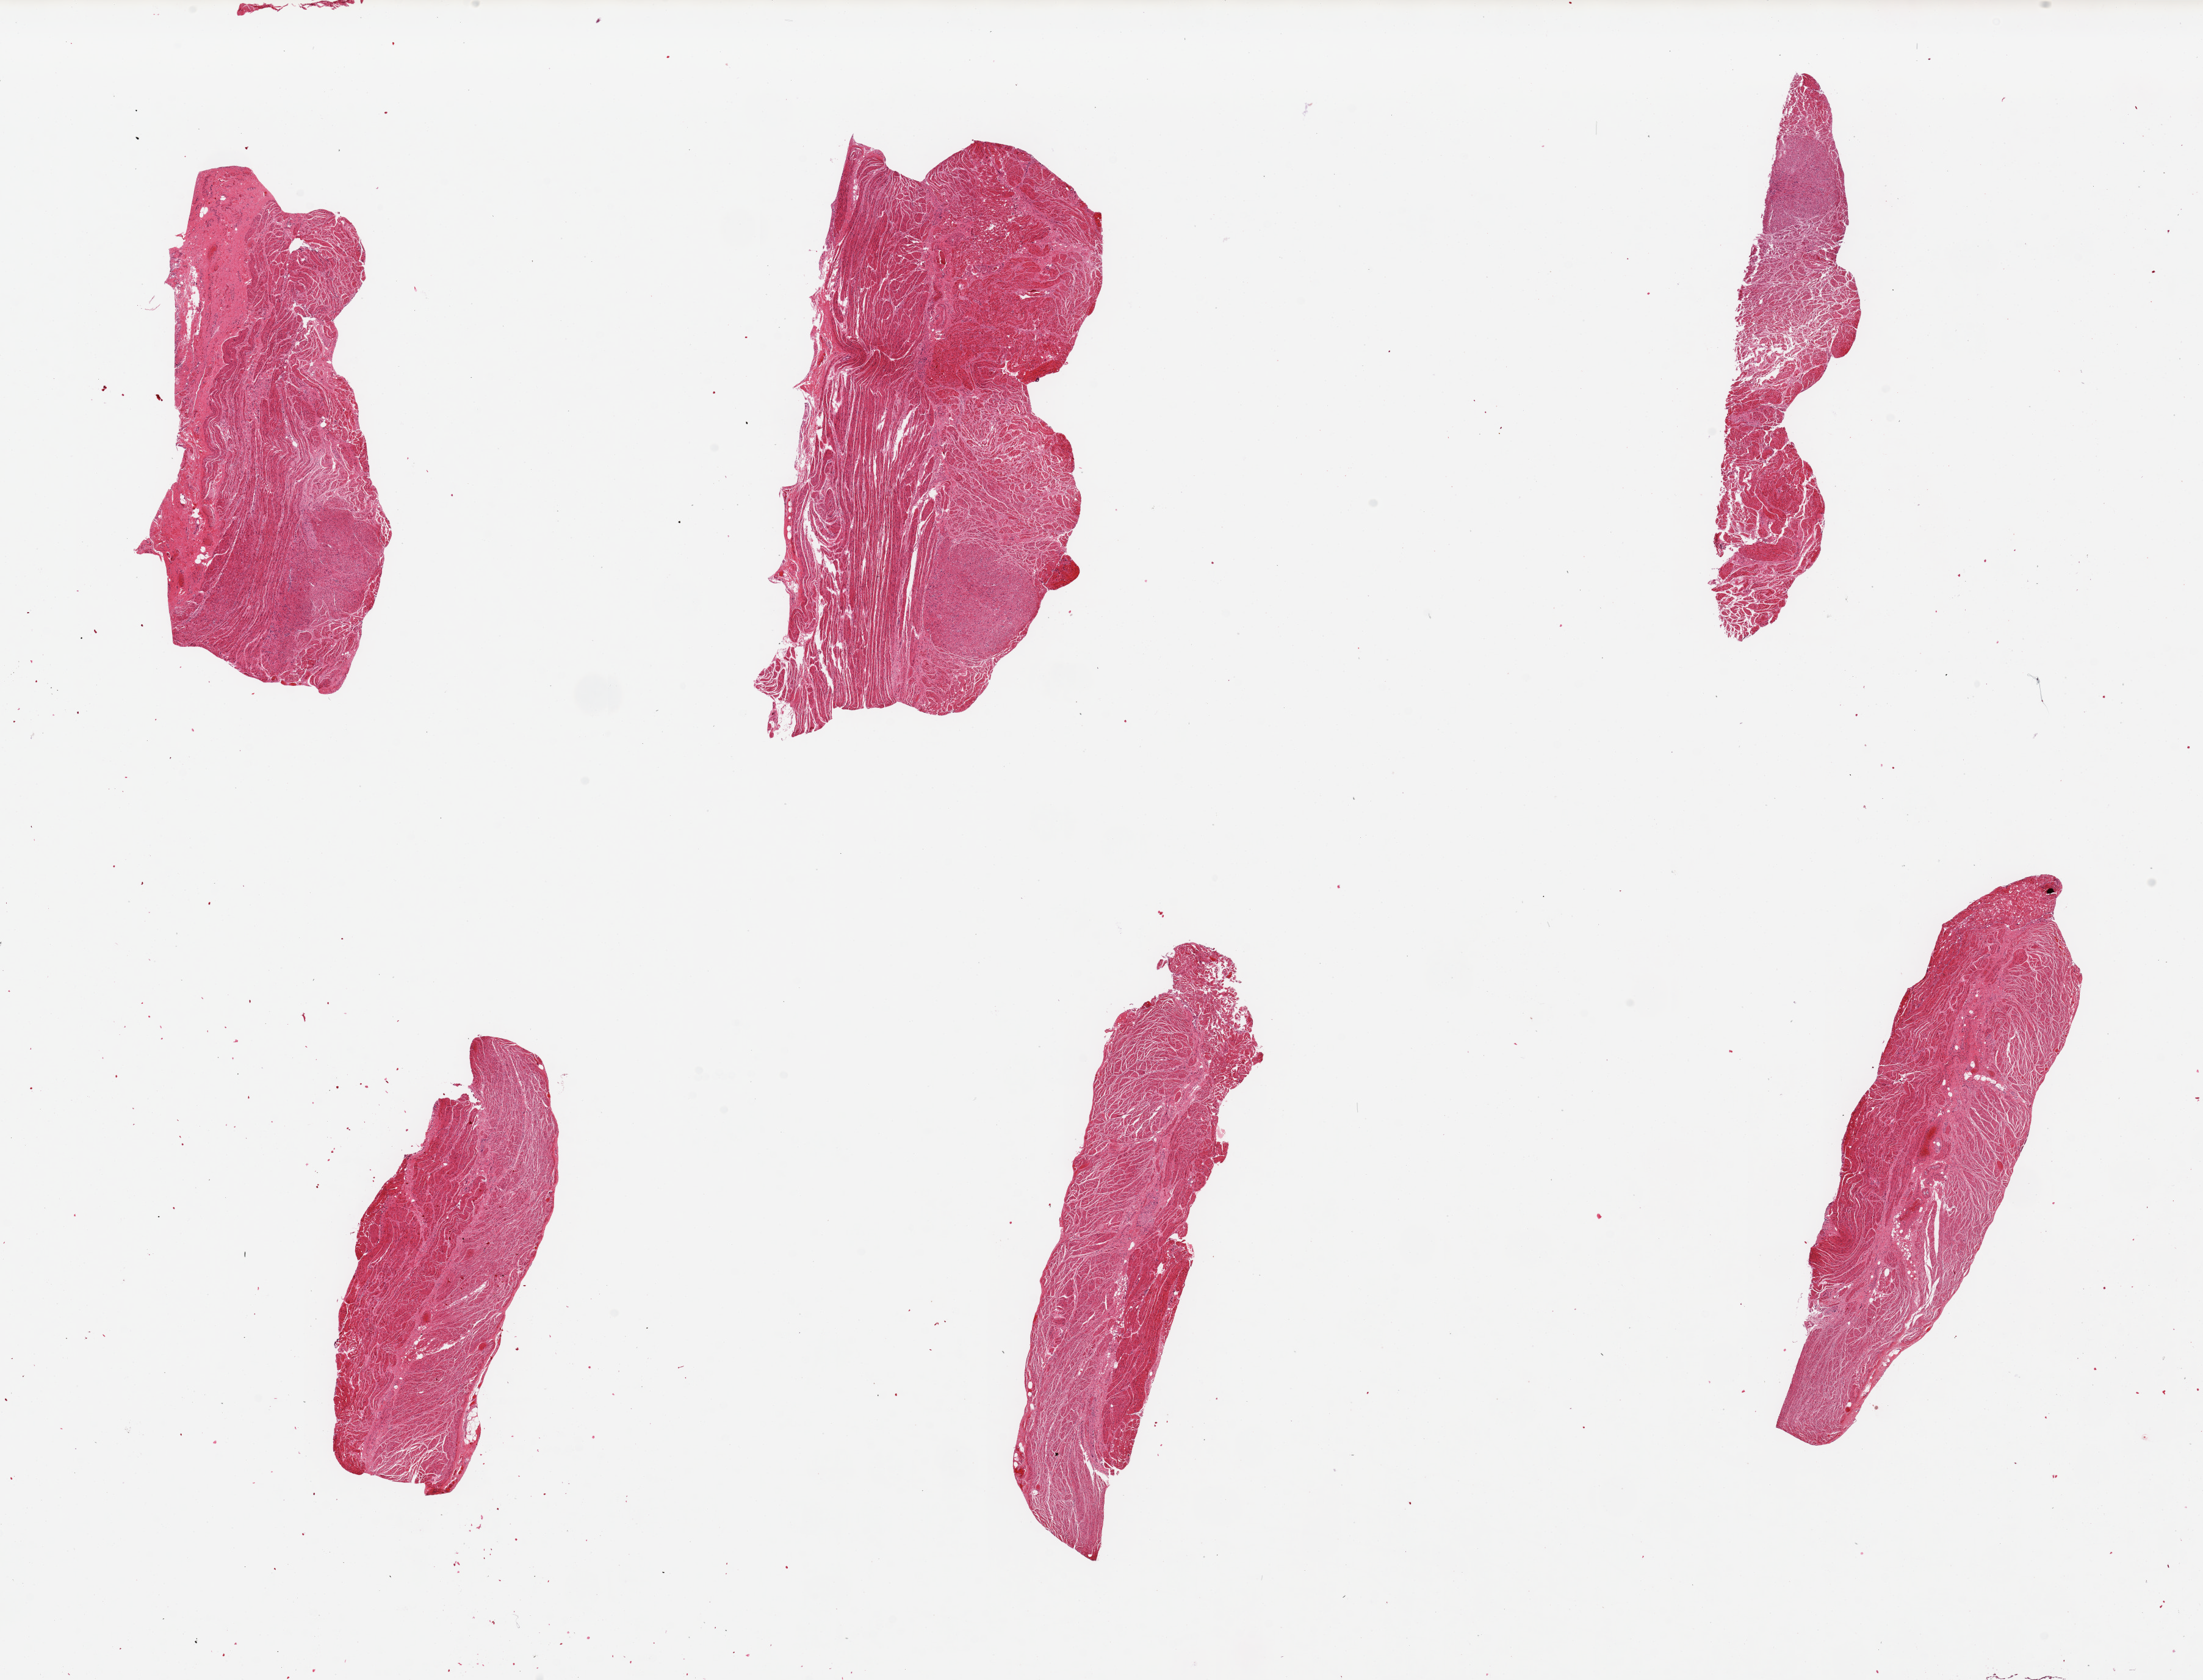
Digitized hematoxylin and eosin (H&E)-stained section — shown as a low-resolution overview of the whole scanned area (about 28.5 x 21.8 mm); PAXgene-fixed, paraffin-embedded tissue; sampled site (target tissue): gastroesophageal junction; donor tissue sample. Male donor.
Review note (as recorded): 6 pieces ~7x3mm. All muscle, well preserved.